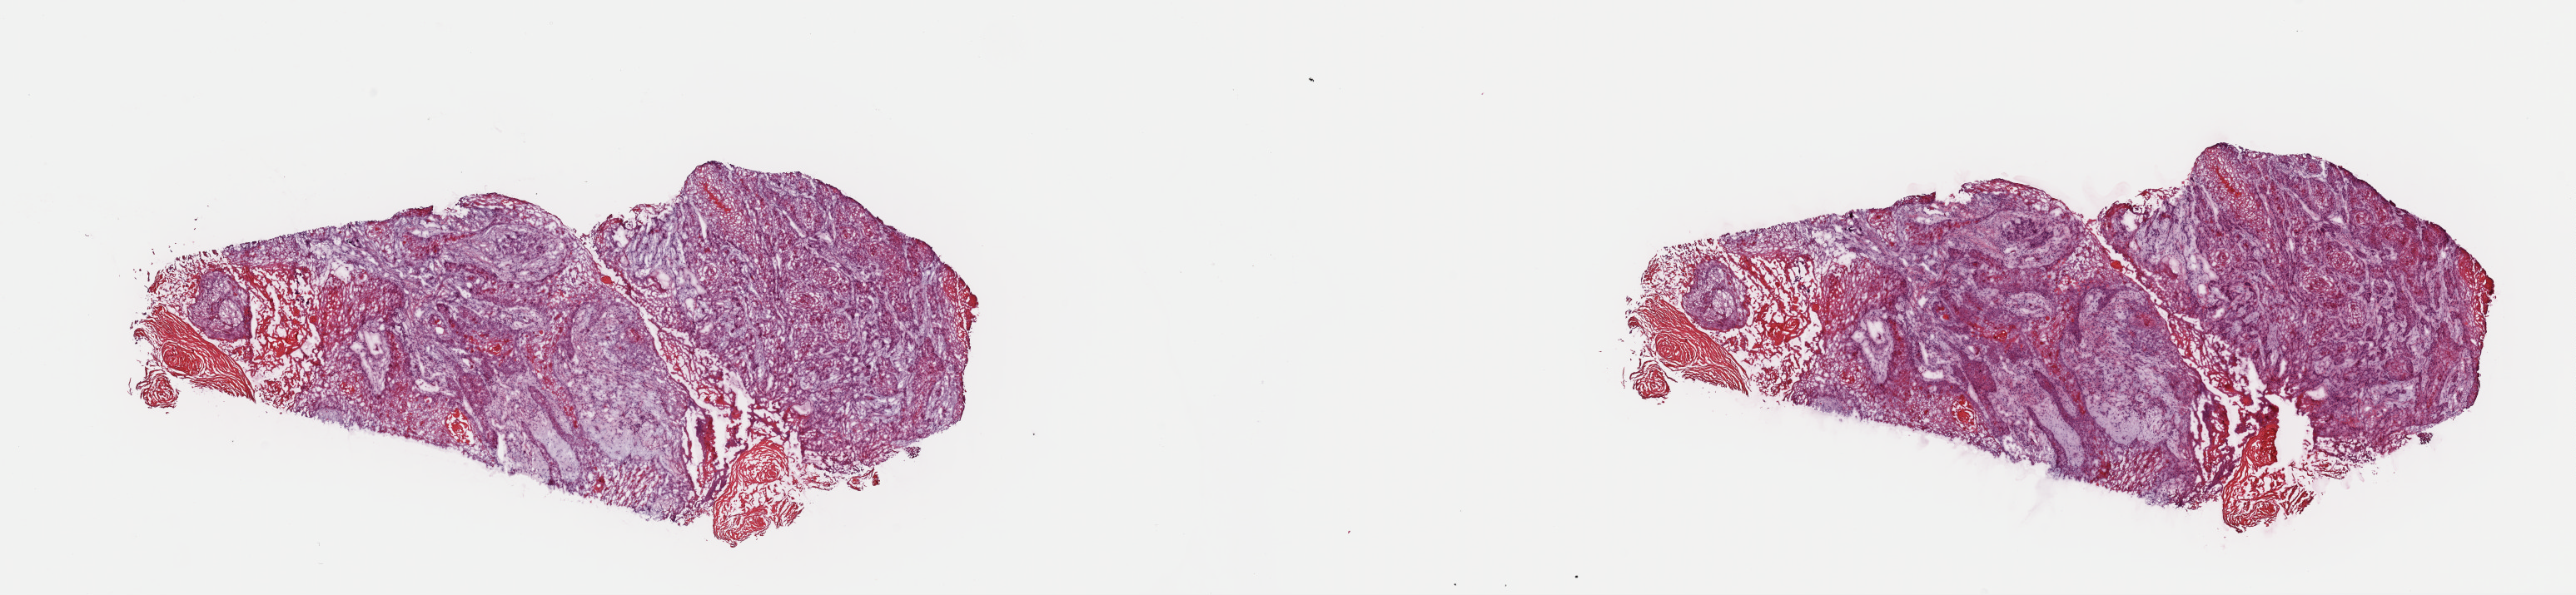
H&E-stained whole-slide image, low-resolution overview of the scanned area, about 24.4 x 5.6 mm. Frozen section. Primary tumour sample from the head and neck. Female patient; age at initial diagnosis 65 years. Histologic grade: G2 (moderately differentiated). Composition of this section per pathologist review: tumour cells 100%, tumour nuclei 80%, normal cells 0%, stromal cells 0%, necrosis 0%. Infiltration values recorded for this section: lymphocyte infiltration 4%, monocyte infiltration 0%, neutrophil infiltration 0%.
* laterality: left
* AJCC pathologic stage: IVB
* pathologic diagnosis: Squamous cell carcinoma, NOS (gum, NOS)